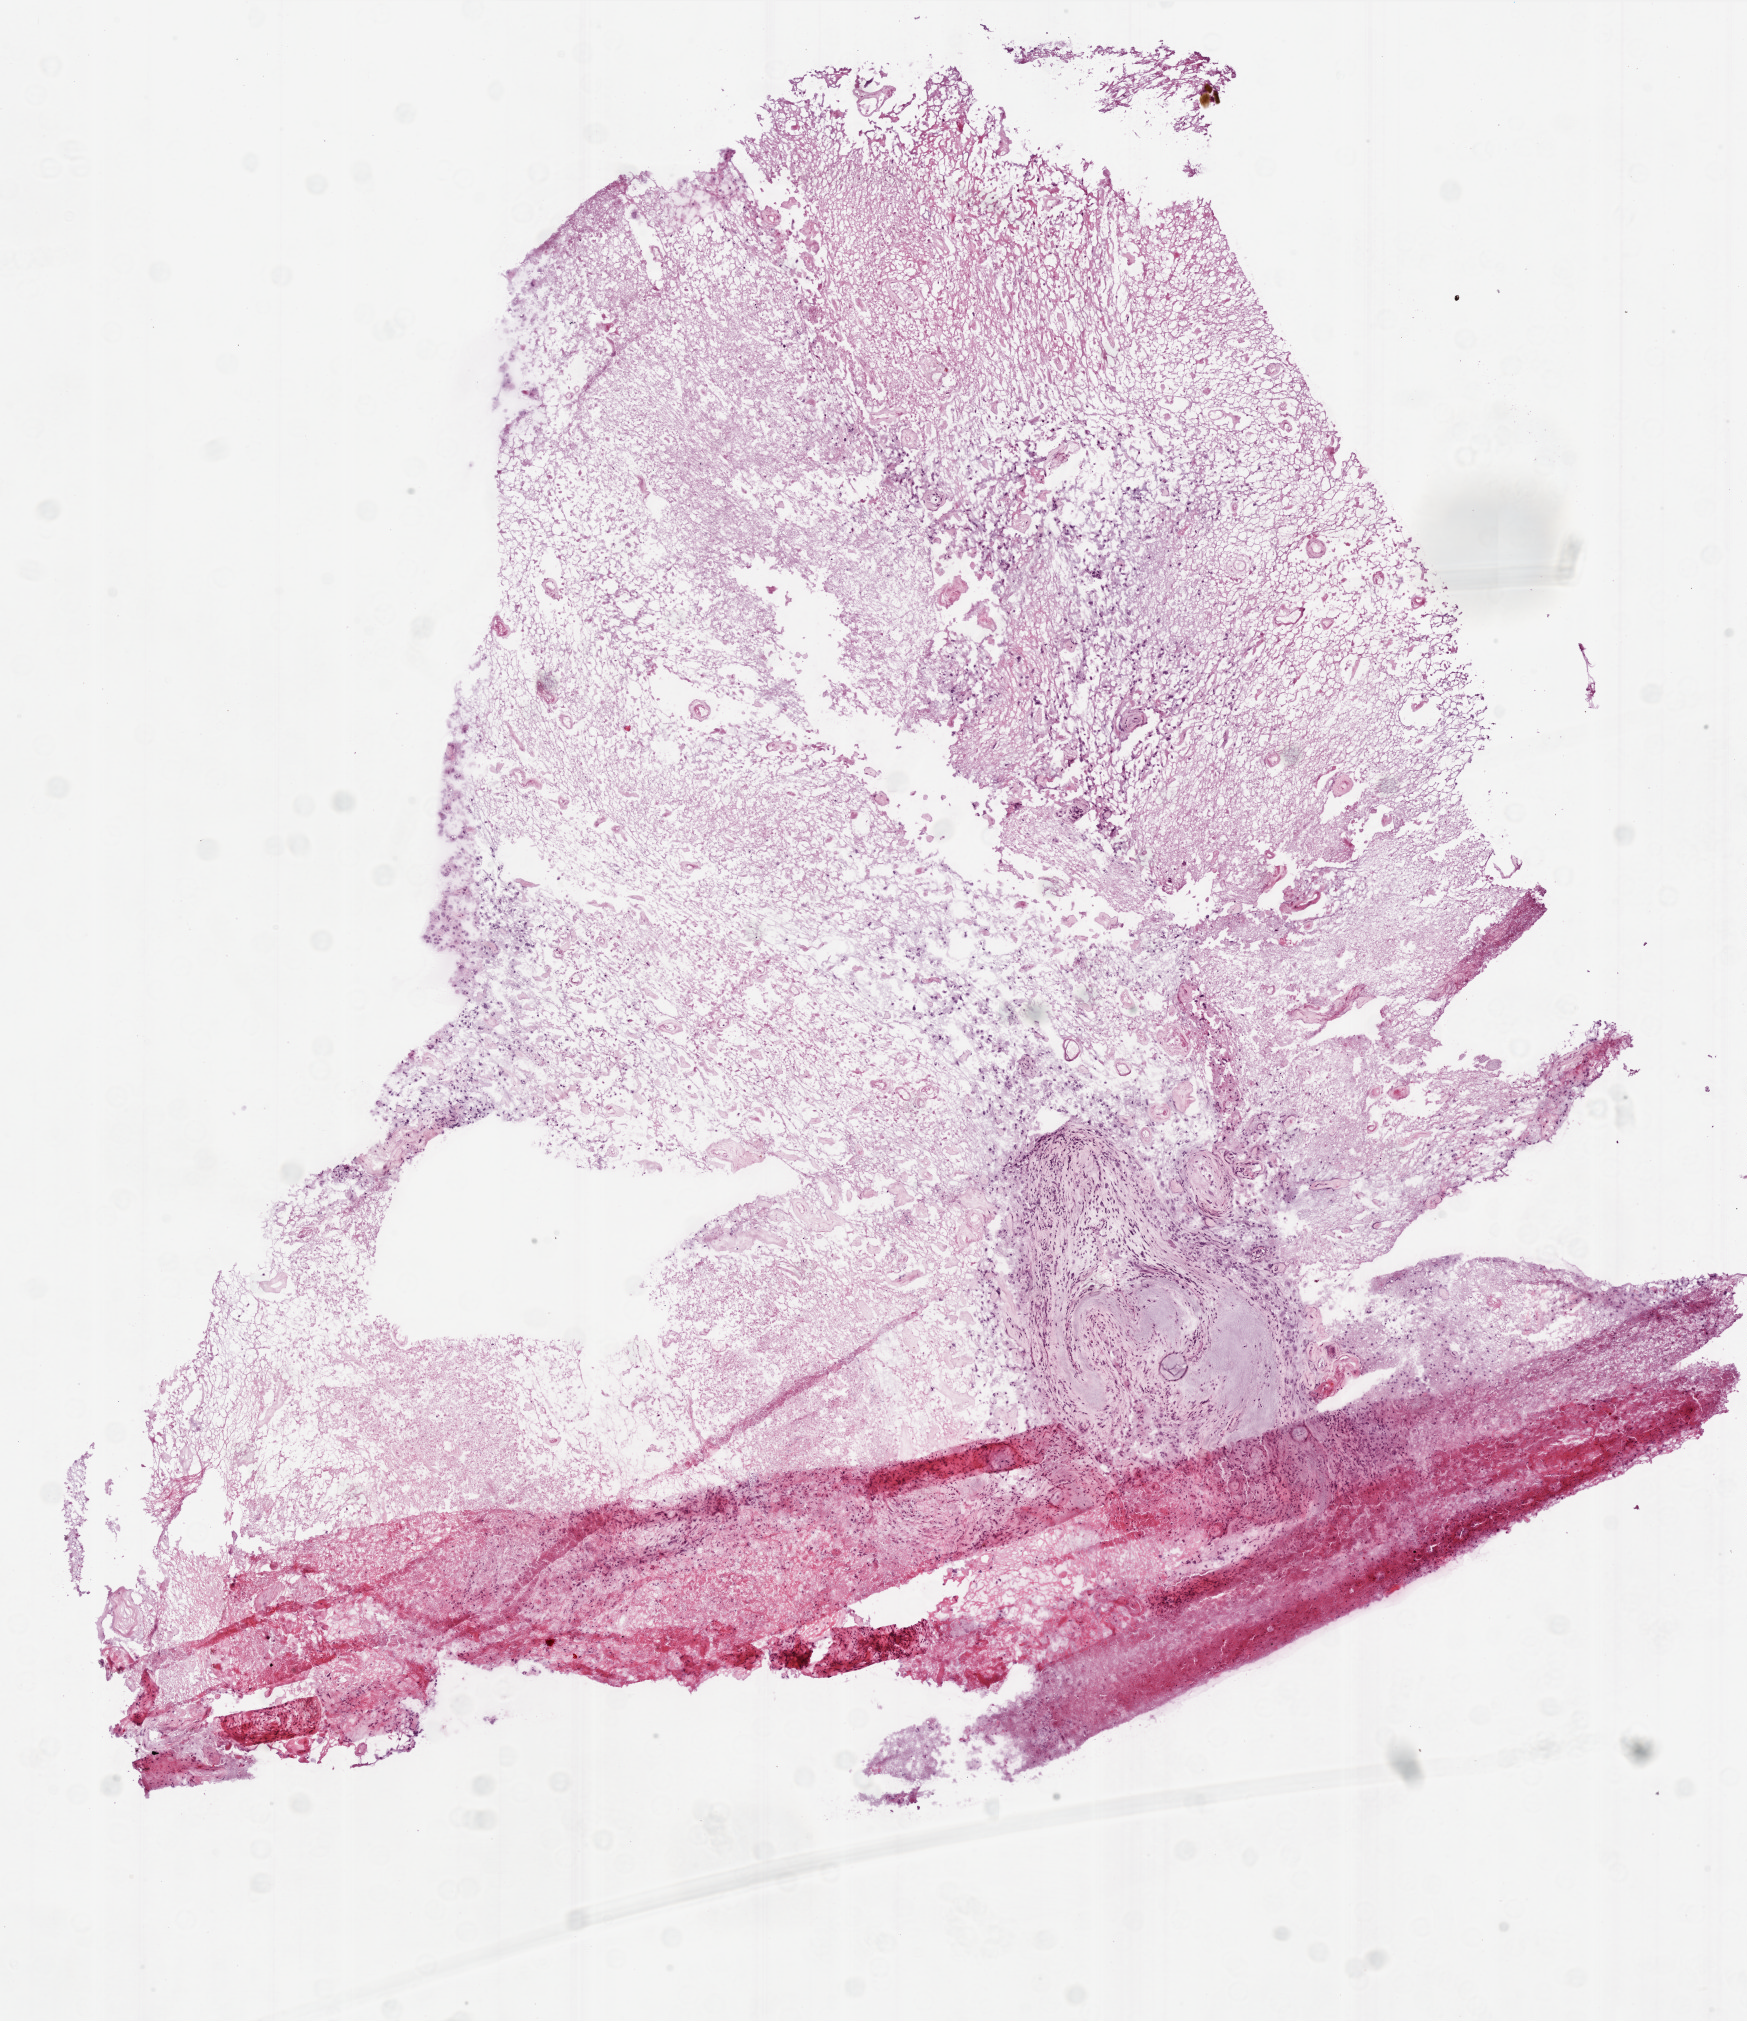
H&E-stained whole-slide image — a low-resolution overview of the entire scanned area, about 7.0 x 8.1 mm. Composition of this section per pathologist review: tumour cells 5%, tumour nuclei 100%, normal cells 0%, stromal cells 0%, necrosis 95%.
Specimen: frozen section; primary tumour sample from the brain.